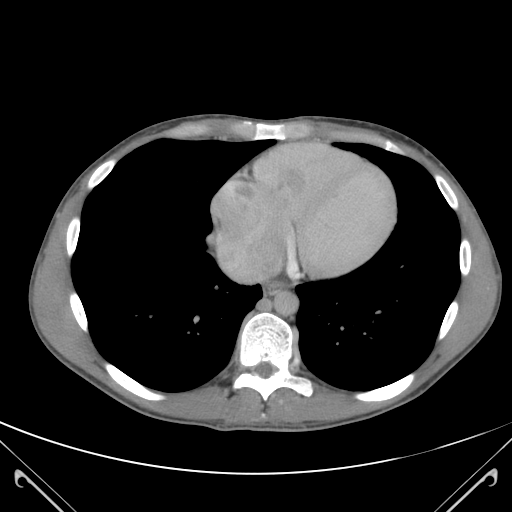
Contrast-enhanced abdominal CT (liver protocol), one axial slice; position 113 of 118 along the scan axis; soft-tissue window (W 400 / L 40 HU); 3 mm slice thickness; 512 × 512 image matrix, field of view 380 × 380 mm. From the clinical record (not read from this slice): diagnosis: hepatocellular carcinoma (patient treated with transarterial chemoembolisation; whether this scan precedes or follows treatment is not stated here); TNM stage (as recorded): Stage-IIIB; Child-Pugh class: A; tumour nodularity: uninodular.
Outlined on this slice (semi-automatically segmented with operator editing):
- abdominal aorta: bounding box (x1, y1, x2, y2) in pixels: (274, 291, 298, 314)